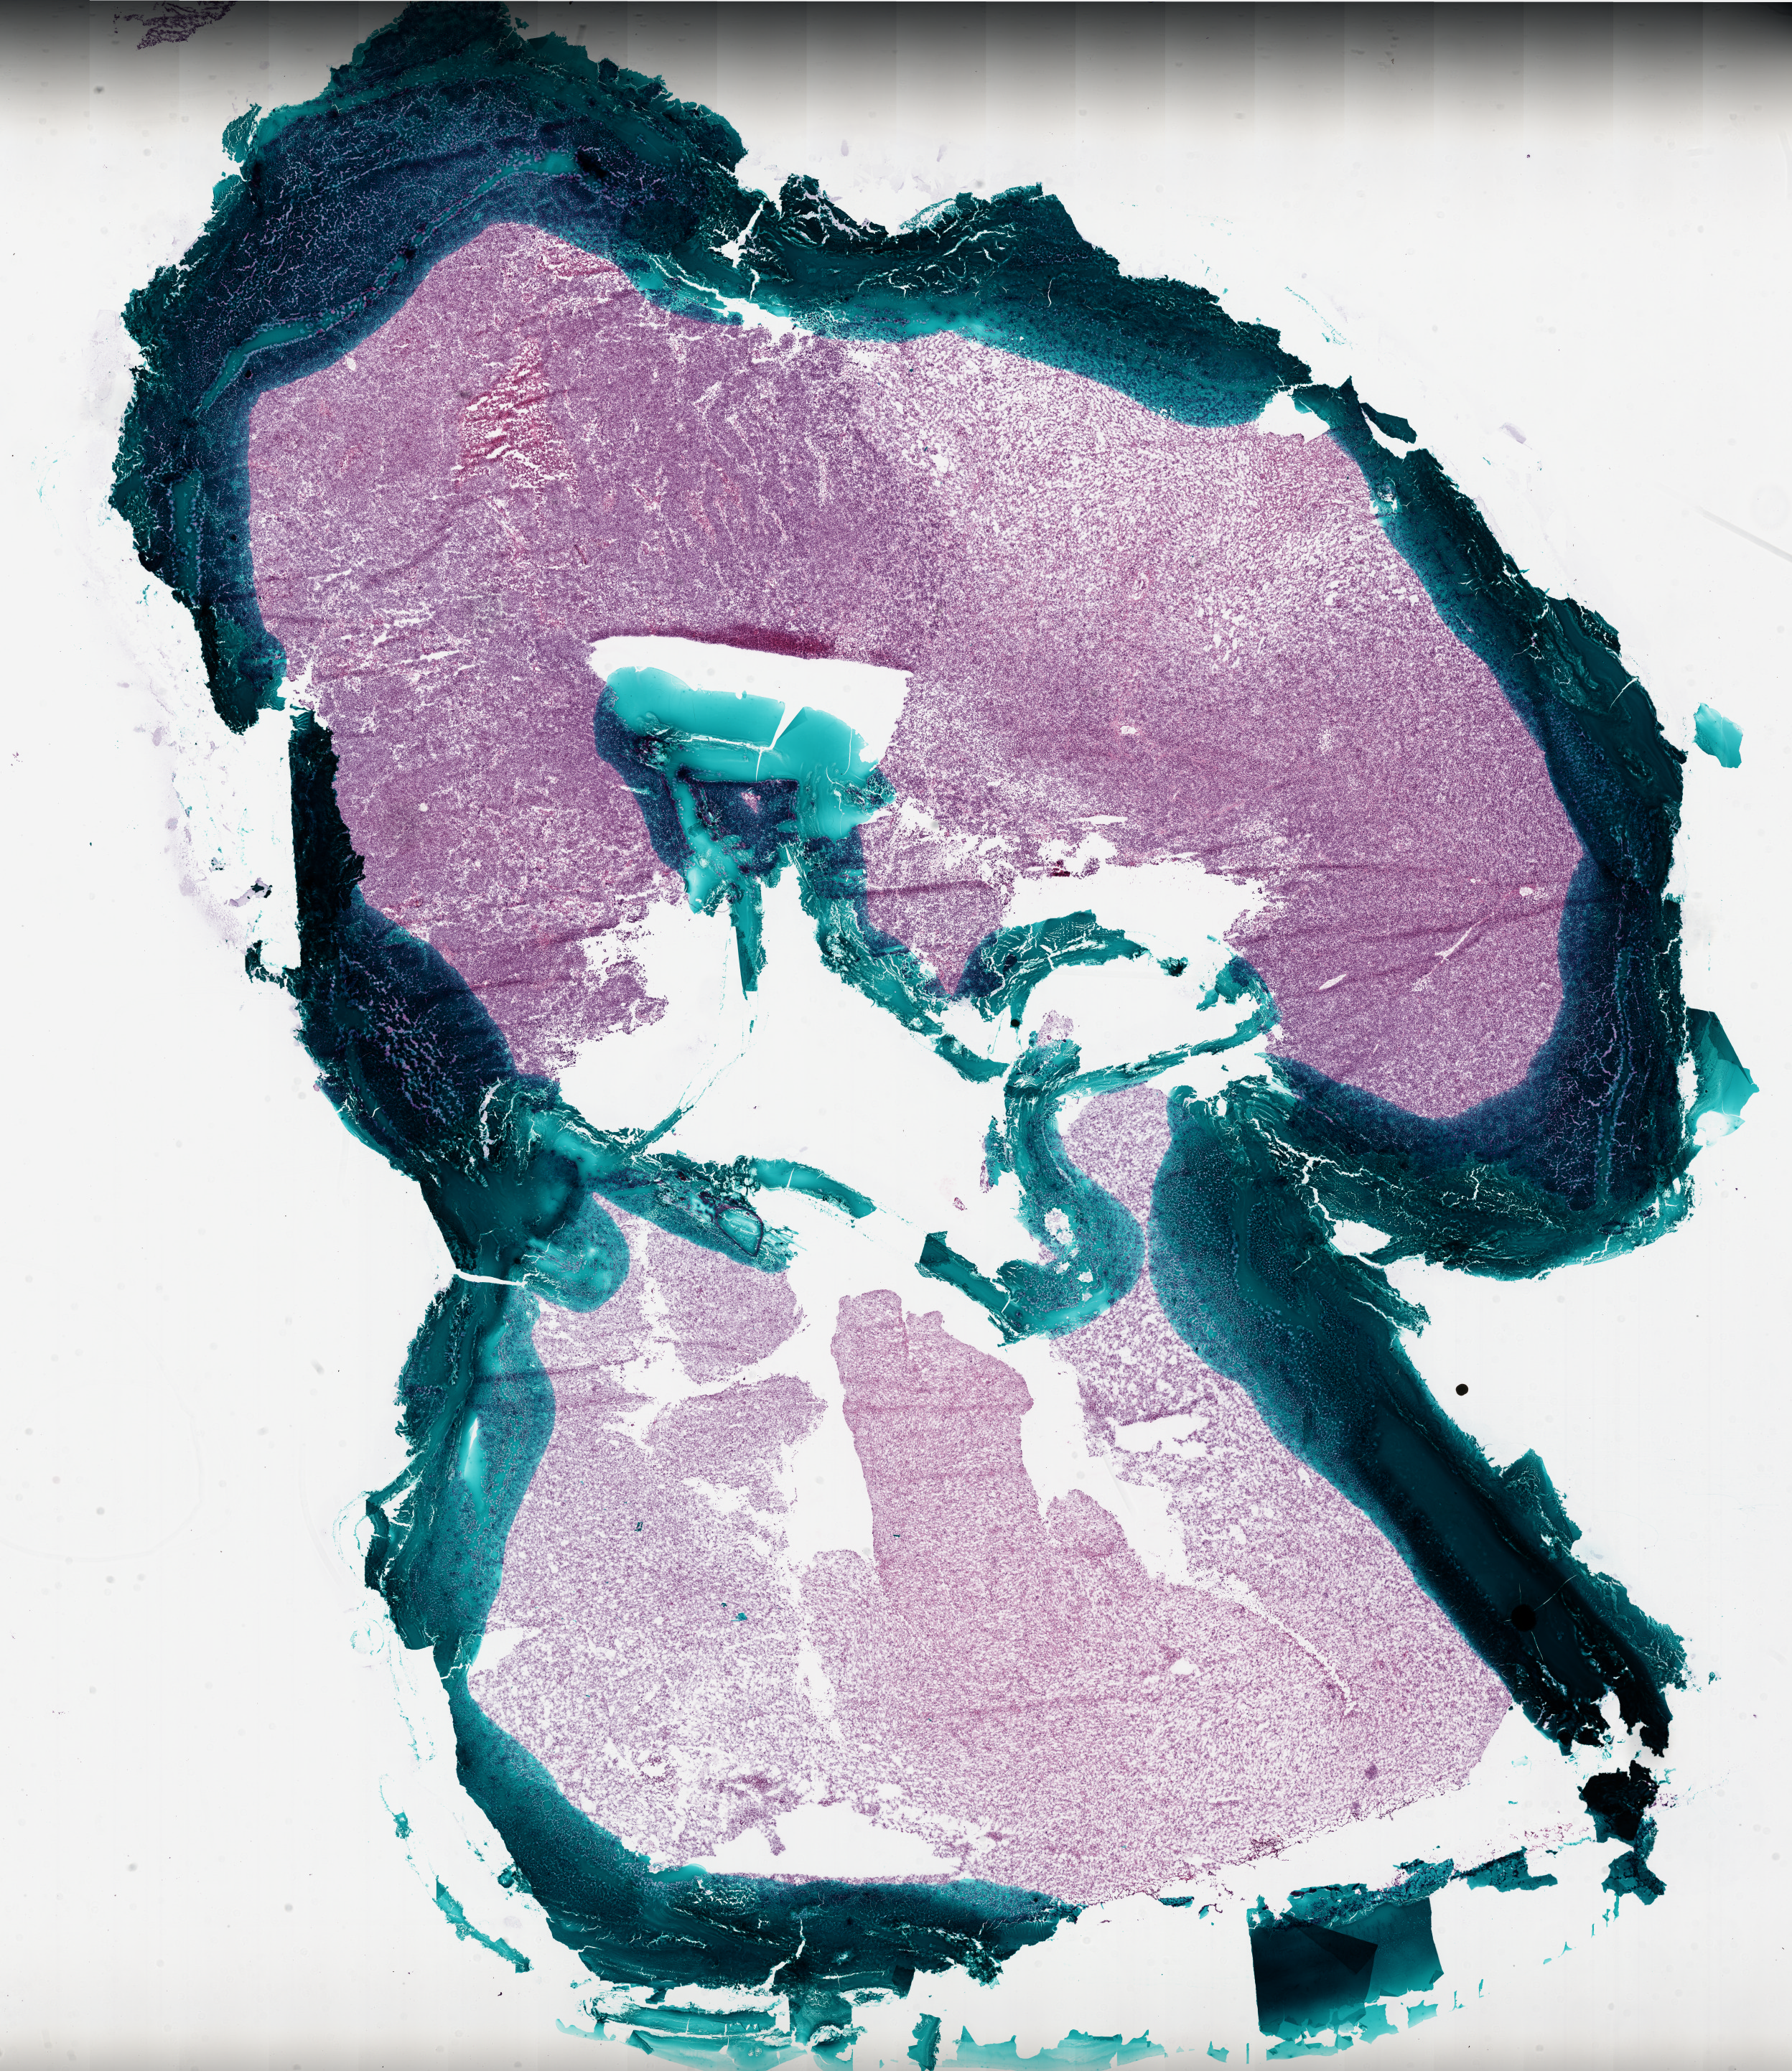
Whole-slide histology image, Hematoxylin and eosin (H&E) stained, low-resolution overview of the scanned area, about 20.0 x 23.1 mm (slide scanned at 20x); frozen section from the bottom of the tissue portion; brain, primary tumour sample. Female patient; age at initial diagnosis 29 years. Composition of this section per pathologist review: tumour cells 95%, tumour nuclei 100%, normal cells 0%, stromal cells 0%, necrosis 5%.
- diagnosis: Glioblastoma